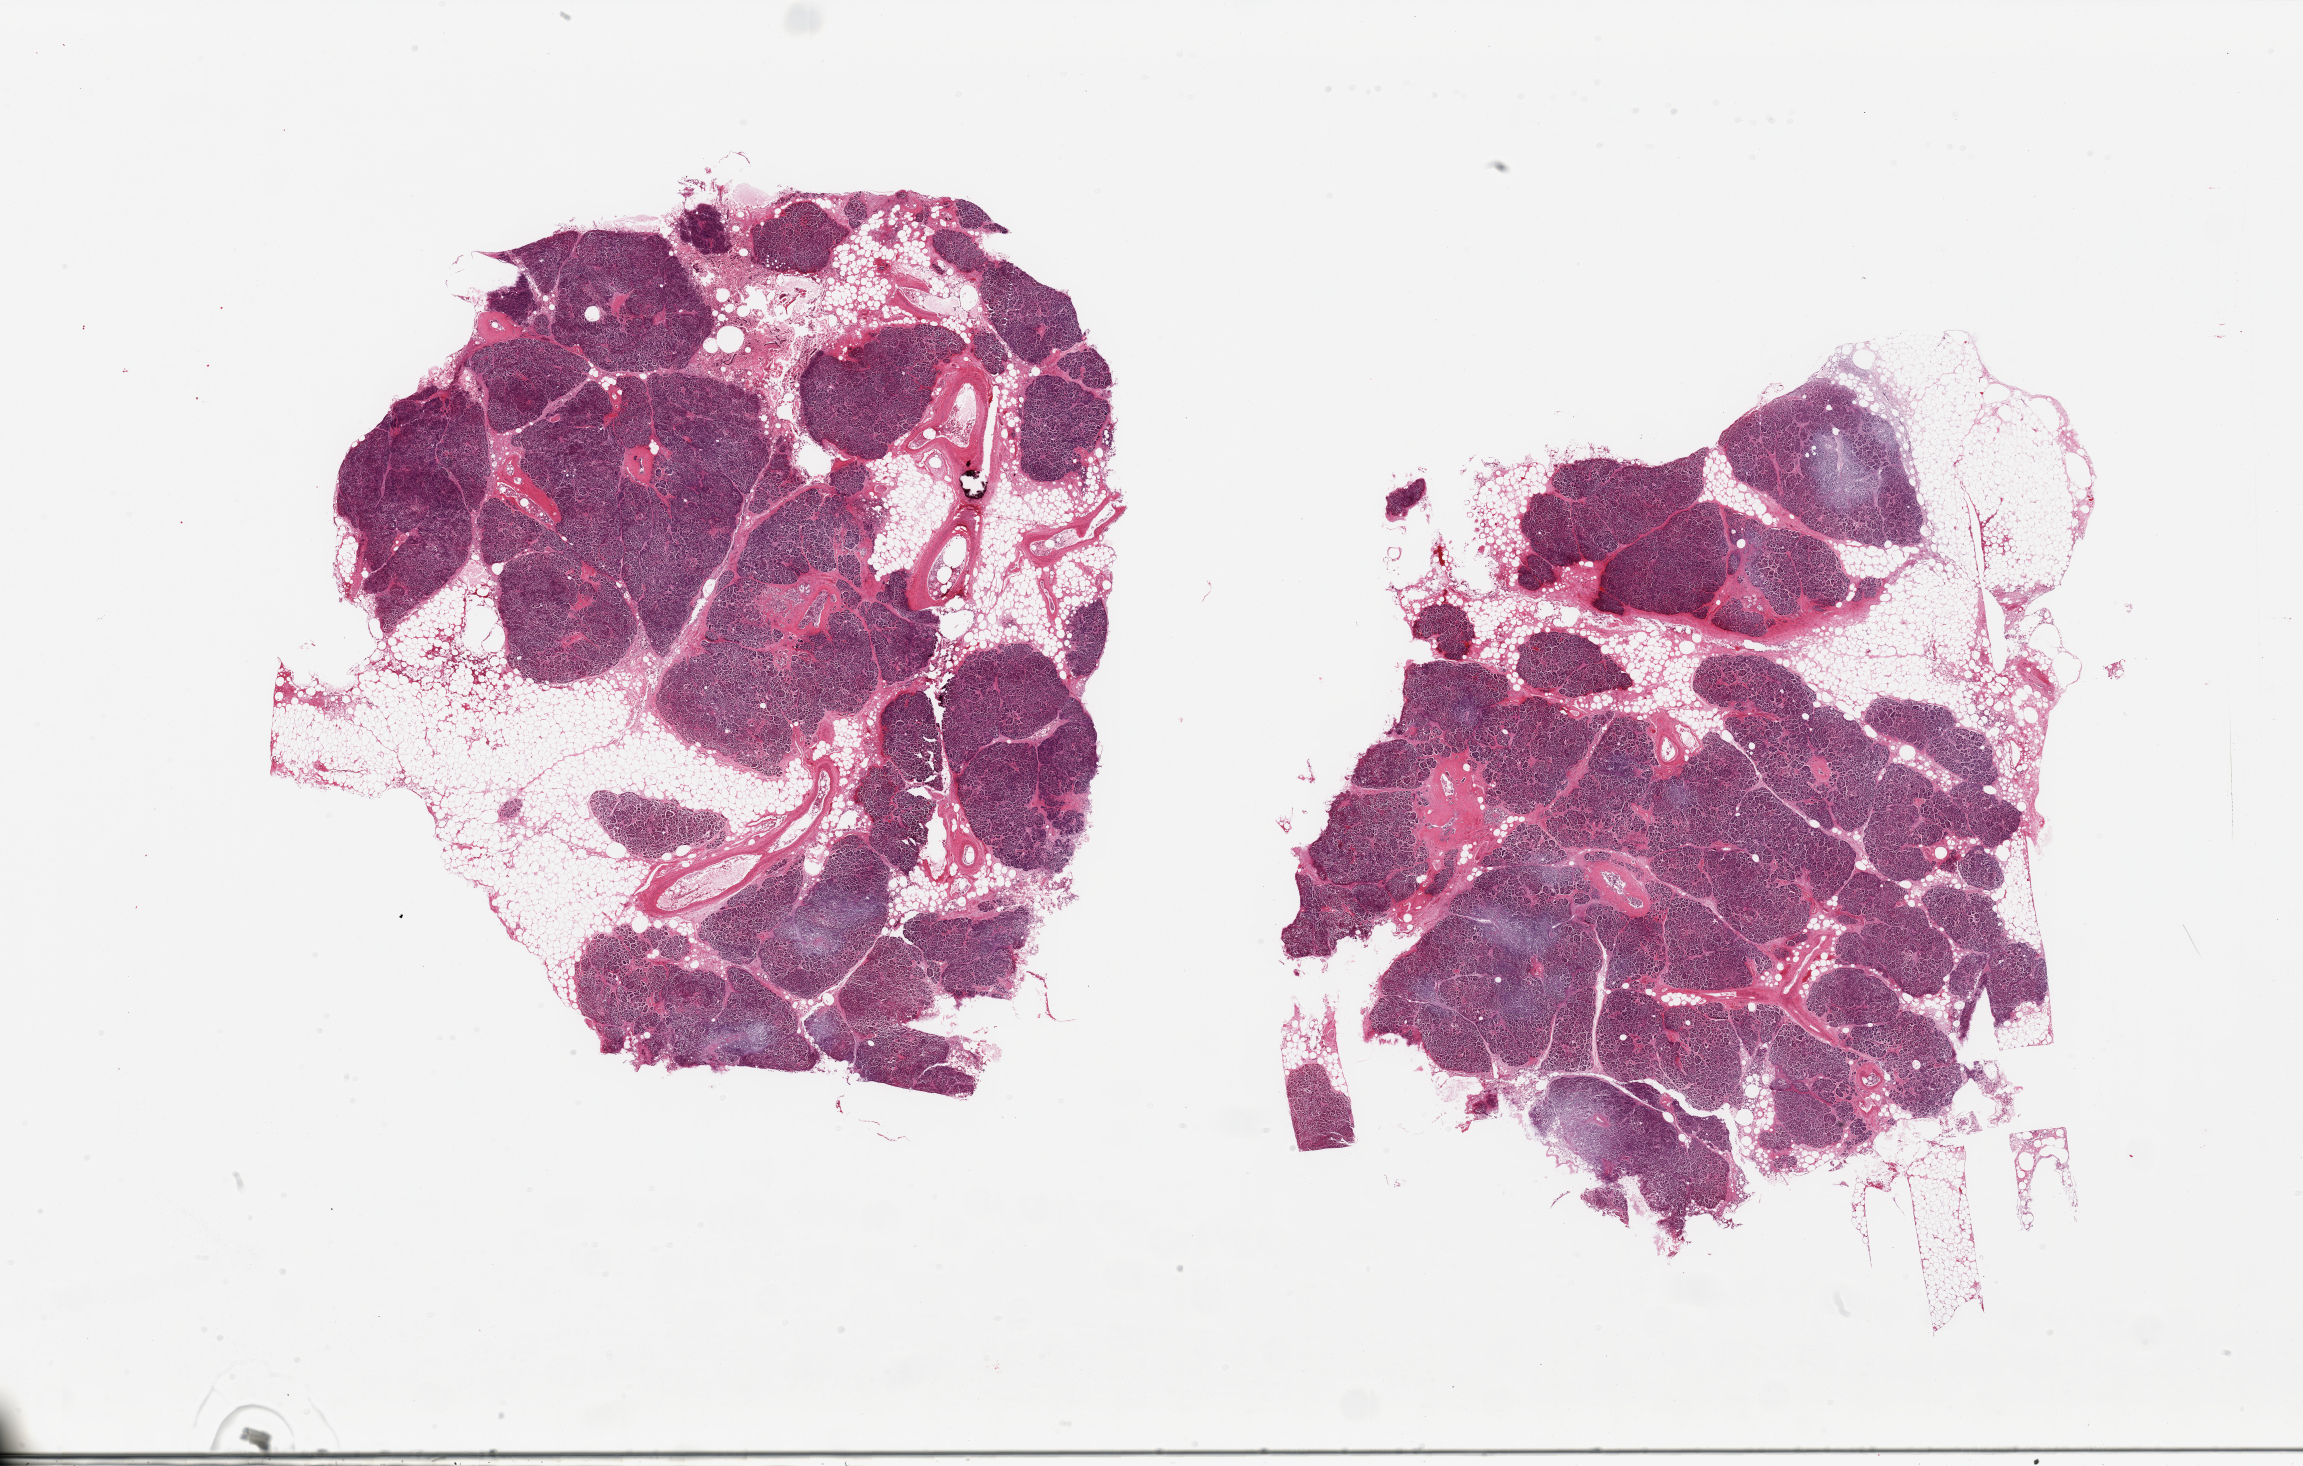
Haematoxylin and eosin whole-slide image, whole scanned area (about 36.4 x 23.2 mm) shown as a low-resolution overview, PAXgene-fixed, paraffin-embedded tissue, target tissue: pancreas, tissue donor sample. Male donor.
Review note (as recorded): 2 pieces; moderate to severe parenchymal and septal fat autolysis; ~50% and ~30% internal/external fat; thick-walled vessels with calcification; rare Langerhans islets observed.